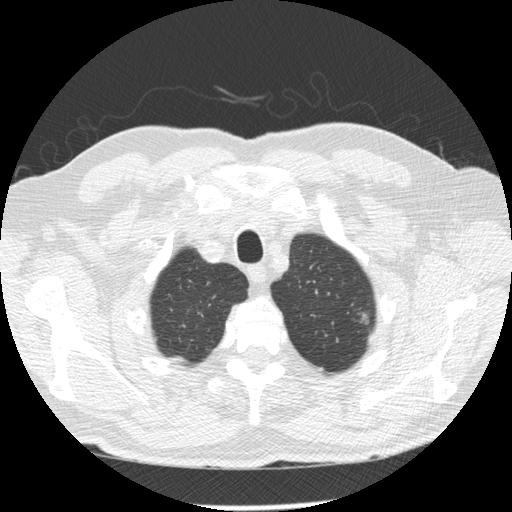
Low-dose screening chest CT, one axial slice; position 233 of 258 along the scan axis; reconstruction kernel STANDARD; 120 kVp; lung window (W 1500 / L -600 HU); 2.5 mm slice thickness; 512 × 512 image matrix.
Structures marked on this image (expert manual segmentation):
- lesion 1 (tumor, upper lobe of left lung): bounding box (x1, y1, x2, y2) in pixels: (359, 311, 370, 337)